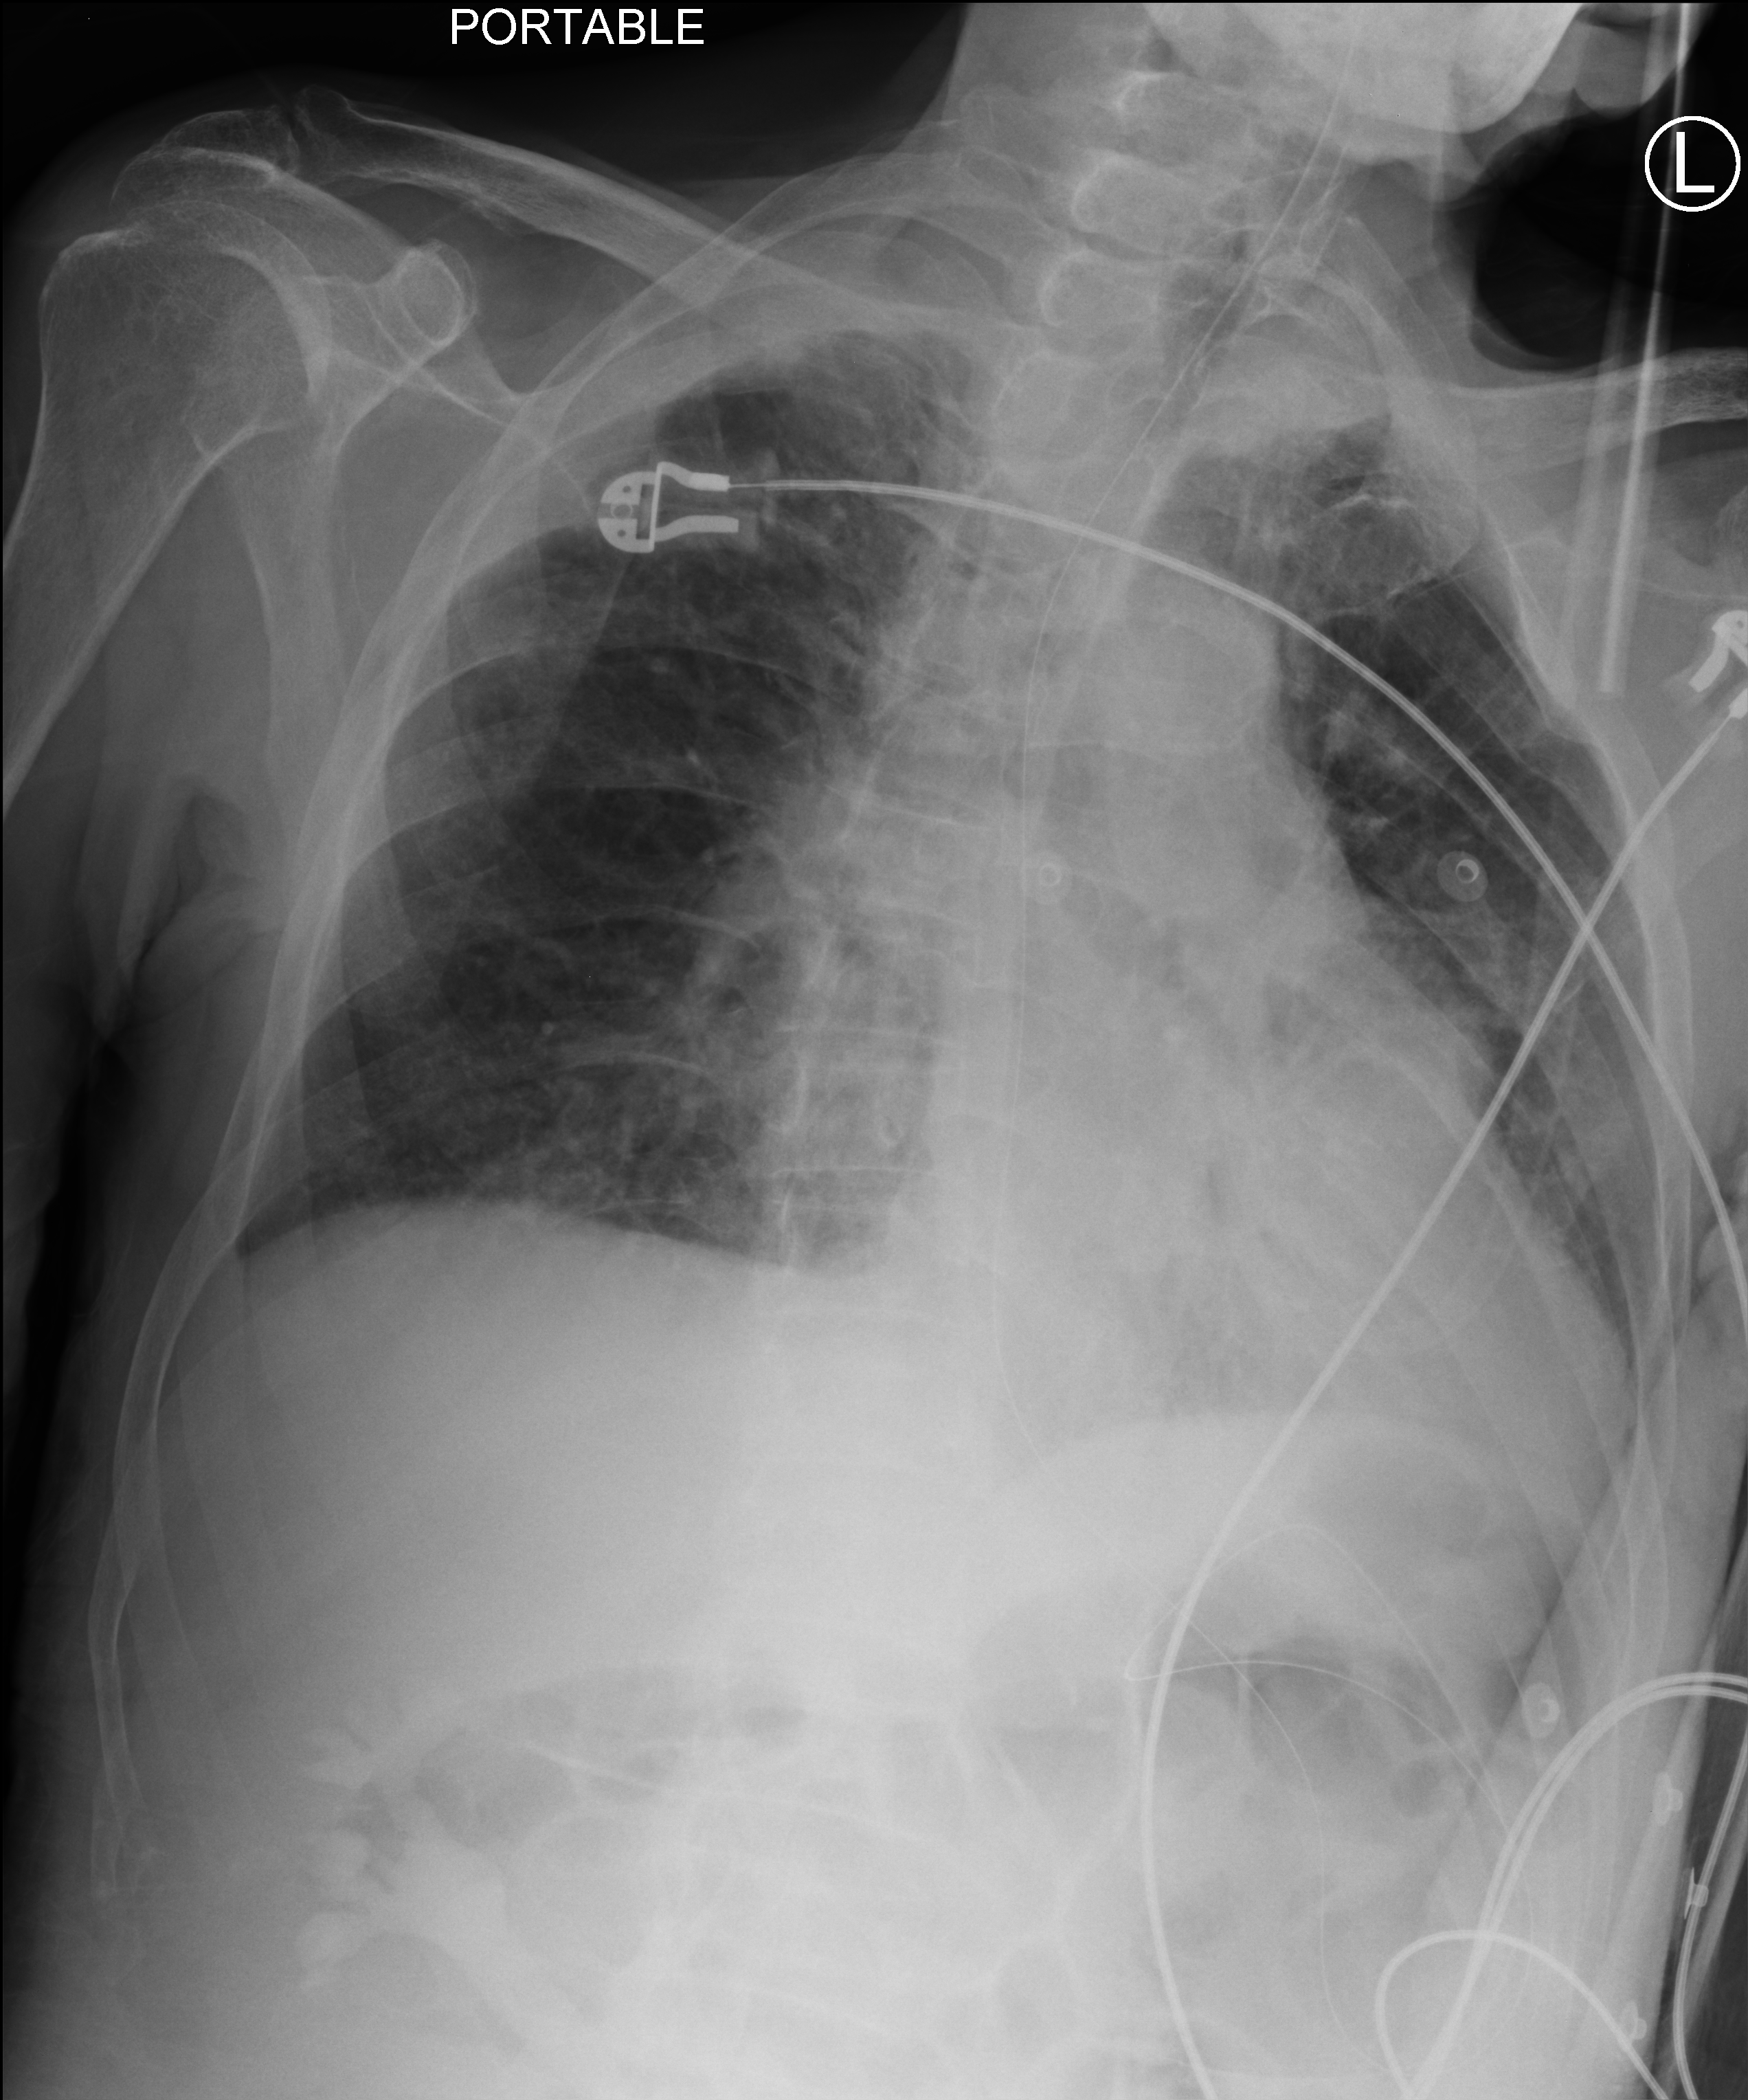
Bedside chest radiograph (computed radiography), anteroposterior (AP) projection. Patient hospitalised with COVID-19; male, aged 75–90 years.
From the hospital-stay record, not from the radiograph (when in the stay this image was taken is not recorded): admitted to intensive care during this hospital stay: no; mechanically ventilated during this hospital stay: no; smoking status (admission record): former.